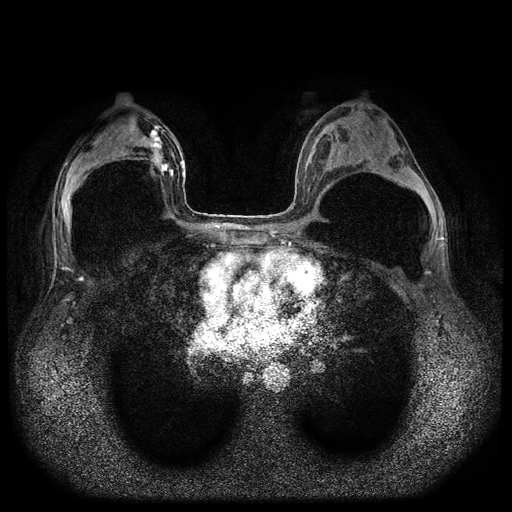
Breast MRI (dynamic contrast-enhanced, multi-phase), one axial slice. Position 48 of 116 along the scan axis. Dynamic contrast-enhanced series, time point 2 of 5 at this slice position (early post-contrast). 1.5 T. TE 2.6 ms, TR 5.4 ms. 512 × 512 image matrix. Female patient, age 42 years.
Outlined on this slice (semi-automatically segmented with operator editing):
- breast lesion (labelled 'tumour' in the annotation; benign lesions carry a separate 'benign' label): box from (x=150, y=127) to (x=174, y=181) px